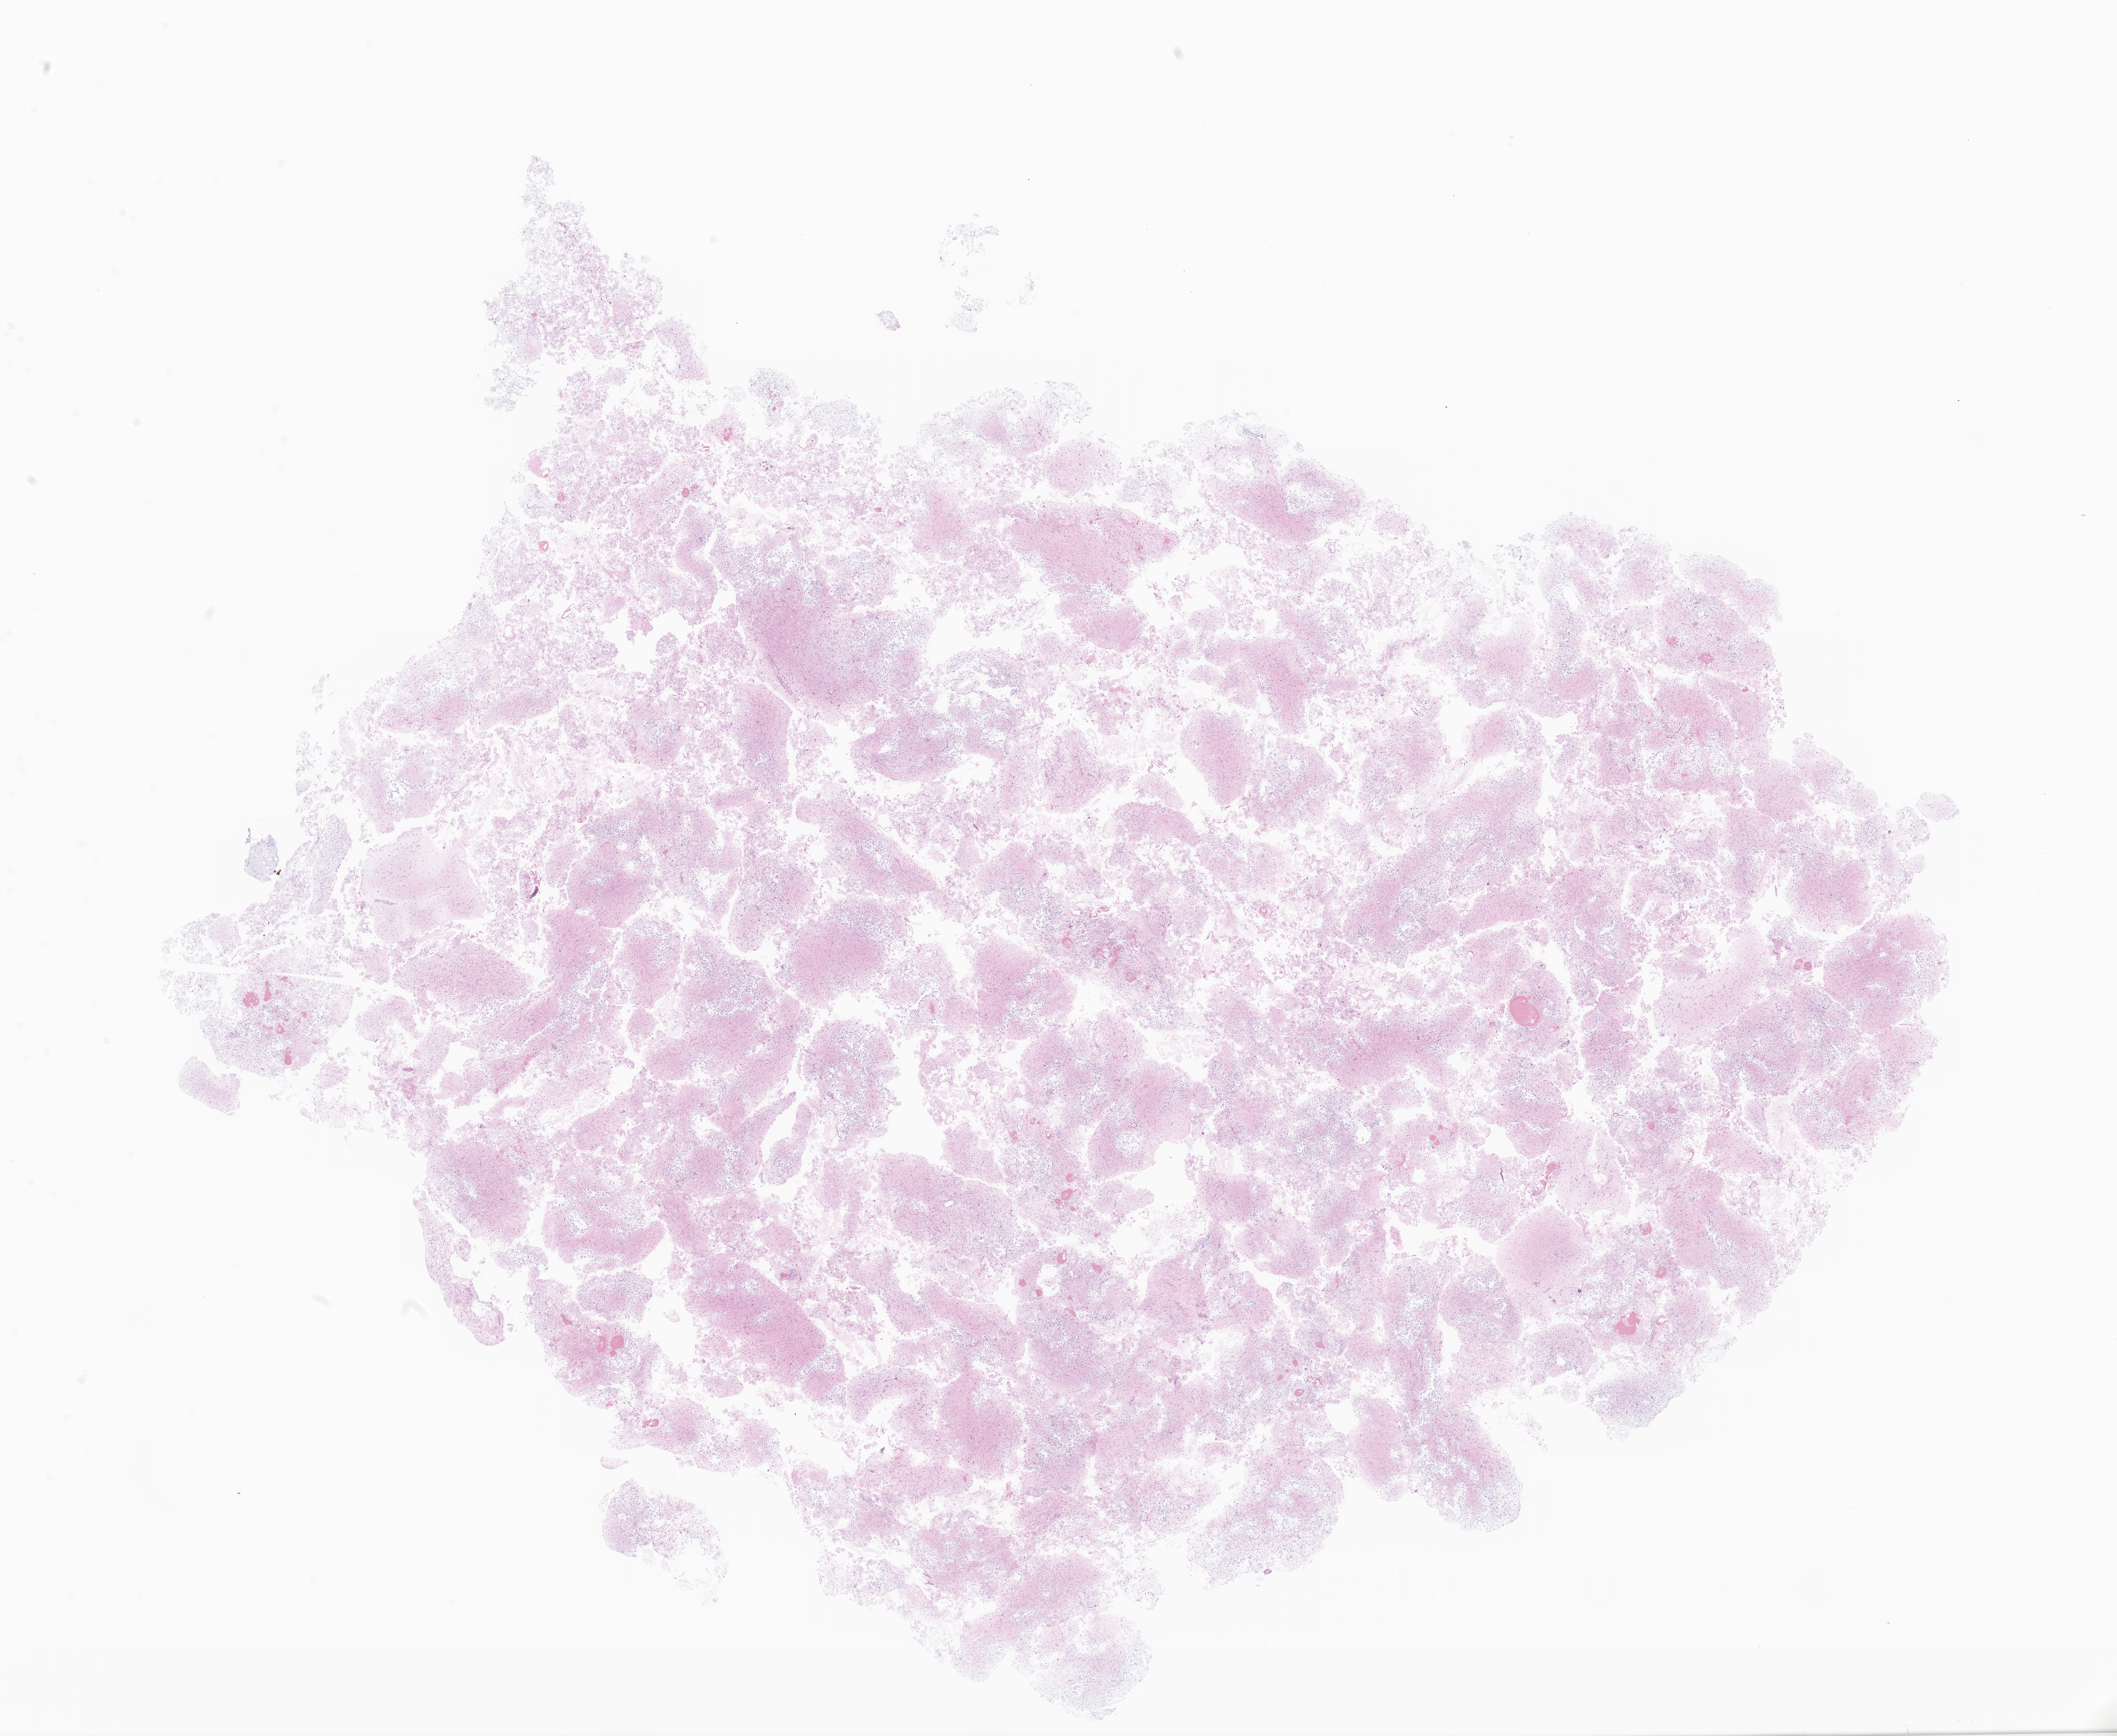
Whole-slide image, hematoxylin and eosin (H&E) stain of tumor tissue from the brain, a low-resolution overview of the entire scanned area, about 24.5 x 20.1 mm; FFPE section. Male patient, age 186 months (15 years 6 months).
Recorded diagnosis: Pilocytic astrocytoma.